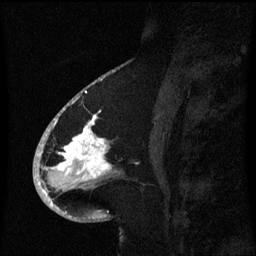
Breast MRI (dynamic contrast-enhanced), one sagittal slice. Slice 31 of 60 in the series (ordered by position). Dynamic contrast-enhanced series, image 2 of 3 at this slice position (ordered by acquisition). 1.5 T. TE 4.2 ms, TR 8.4 ms. 2.1 mm slice thickness. 256 × 256 image matrix, field of view 200 × 200 mm. Patient: female, 53 years. From the clinical record (not read from this slice): setting: breast cancer imaged before/during neoadjuvant chemotherapy; receptor status: HR-positive, HER2-negative.
Annotated regions visible in this slice (semi-automatically segmented with operator editing):
- analysis volume of interest (the breast-tissue region the enhancement analysis was run in; not a lesion): bounding box <49,108,120,201> (left, top, right, bottom; pixels)
- tumour enhancement mask (voxels above the 70 % enhancement threshold inside the analysis volume of interest): <57,116,112,179>